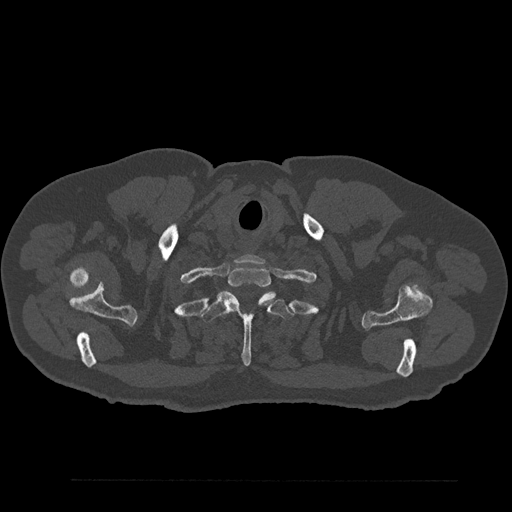
CT including the spine, one axial slice; slice 736 of 797 in the series (ordered by position); 120 kVp; bone window (W 1800 / L 400 HU); 0.5 mm slice thickness; 512 × 512 image matrix, field of view 430 × 430 mm. Male patient, age 61 years. From the clinical record (not read from this slice): primary cancer: prostate.
Structures marked on this image (semi-automatically segmented with operator editing):
- T1 vertebra: bounding box [x1, y1, x2, y2] px = [228, 266, 271, 287]
- T2 vertebra: [201, 291, 294, 366]